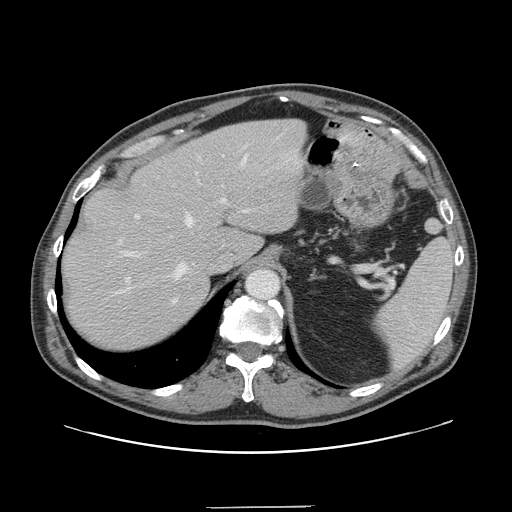
Contrast-enhanced abdominal CT, one axial slice. Slice 110 of 139 in the series (ordered by position). 120 kVp. Intravenous contrast given. Soft-tissue window (W 400 / L 40 HU). 2.5 mm slice thickness. 512 × 512 image matrix, field of view 397 × 397 mm. Male patient, age 64 years. From the clinical record (not read from this slice): diagnosis: colorectal cancer liver metastases, imaged before liver resection; multiple liver metastases: yes; largest metastasis: 3.5 cm; chemotherapy before resection: yes.
Annotated regions visible in this slice (outlined manually by an expert reader):
- hepatic veins: box from (x=124, y=156) to (x=247, y=303) px
- liver: (x=63, y=120)–(x=306, y=349)
- planned liver remnant (the part of the liver to remain after resection): (x=63, y=122)–(x=270, y=349)
- portal vein (with intrahepatic branches): (x=119, y=145)–(x=249, y=289)